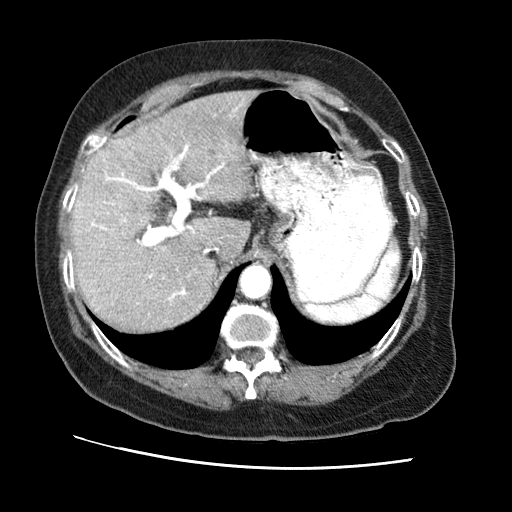
Contrast-enhanced abdominal CT (liver protocol), one axial slice. Slice 46 of 65 in the series (ordered by position). Reconstruction kernel STANDARD. Soft-tissue window (W 400 / L 40 HU). 2.5 mm slice thickness. 512 × 512 image matrix. From the clinical record (not read from this slice): diagnosis: hepatocellular carcinoma (patient treated with transarterial chemoembolisation; whether this scan precedes or follows treatment is not stated here); TNM stage (as recorded): Stage-II; Child-Pugh class: A.
Structures marked on this image (semi-automatic segmentation, software-assisted and operator-edited):
- liver parenchyma outside the tumour (the mass and vessels are separate outlines, so this box may not span the whole liver): bounding box <70,90,257,330> (left, top, right, bottom; pixels)
- liver vessels: <75,145,224,301>